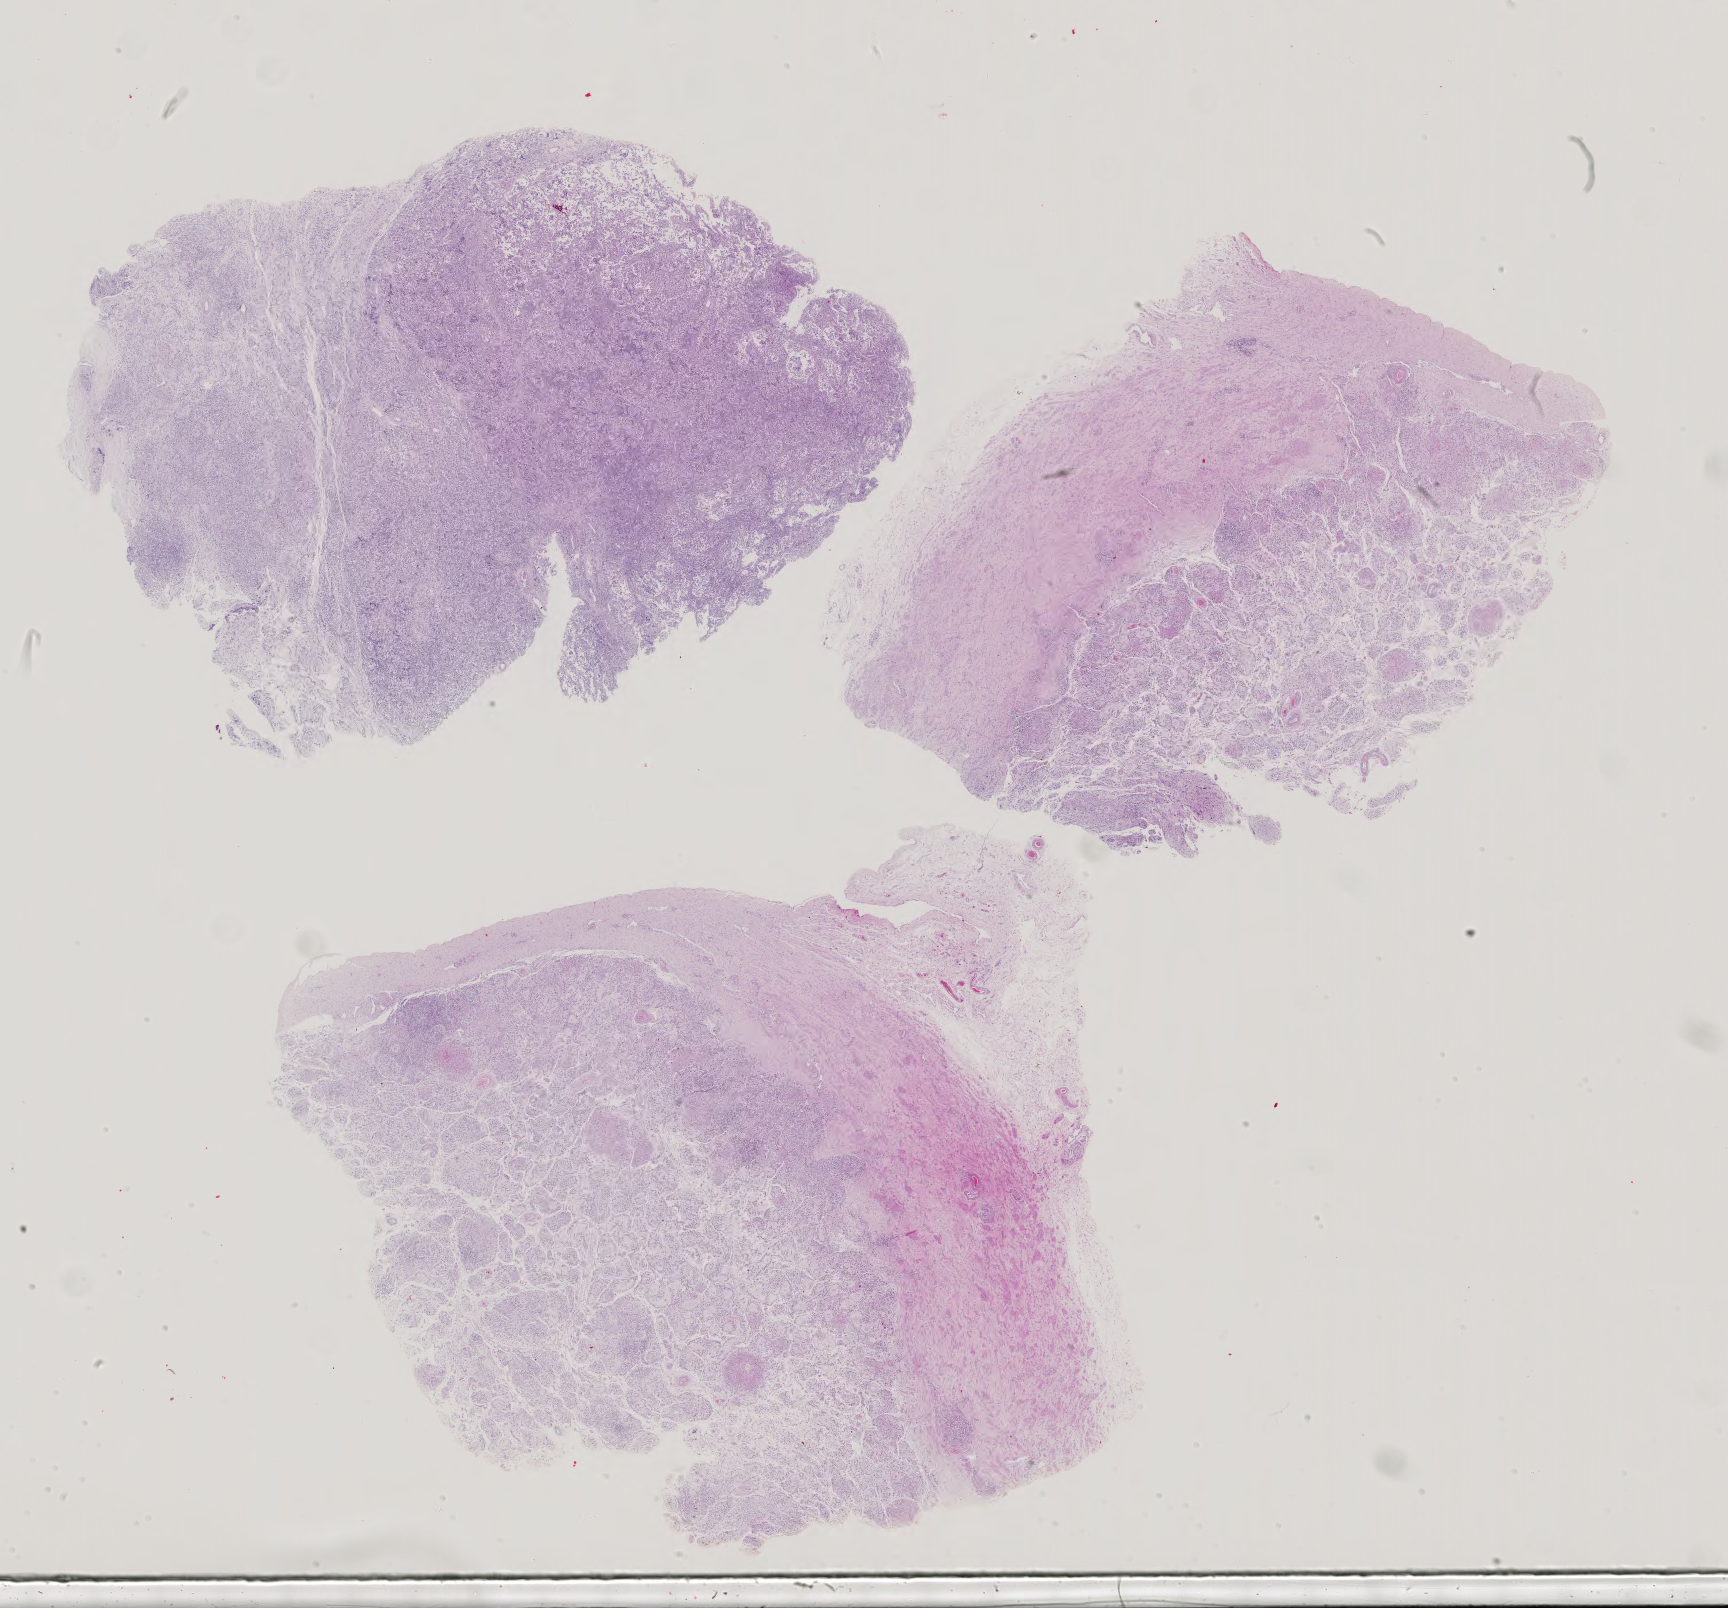
Whole-slide histology image, Hematoxylin and eosin (H&E) stained — shown as a low-resolution overview of the whole scanned area (about 25.2 x 23.4 mm, slide scanned at 40x); formalin-fixed paraffin-embedded (FFPE) diagnostic section; additional new primary tumour sample from the testis. Patient: male, age at initial diagnosis 31 years.
This section: additional new primary tumour. Patient diagnosis: Seminoma, NOS.